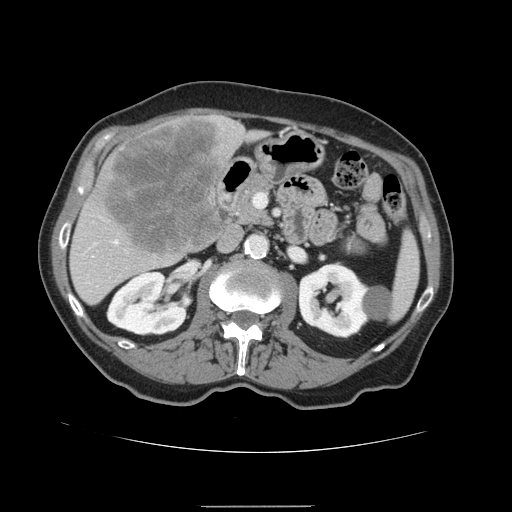
Contrast-enhanced abdominal CT, one axial slice; slice 68 of 168 in the series (ordered by position); 120 kVp; intravenous contrast given; soft-tissue window (W 400 / L 40 HU); 2.5 mm slice thickness; 512 × 512 image matrix, field of view 386 × 386 mm. Male patient, age 74 years. From the clinical record (not read from this slice): diagnosis: colorectal cancer liver metastases, imaged before liver resection; multiple liver metastases: no; largest metastasis: 14.5 cm; disease in both lobes: yes.
Structures marked on this image (outlined manually by an expert reader):
- hepatic veins: box from (x=116, y=241) to (x=118, y=243) px
- liver: (x=69, y=115)–(x=266, y=306)
- planned liver remnant (the part of the liver to remain after resection): (x=73, y=133)–(x=266, y=306)
- liver metastasis: (x=104, y=118)–(x=224, y=260)